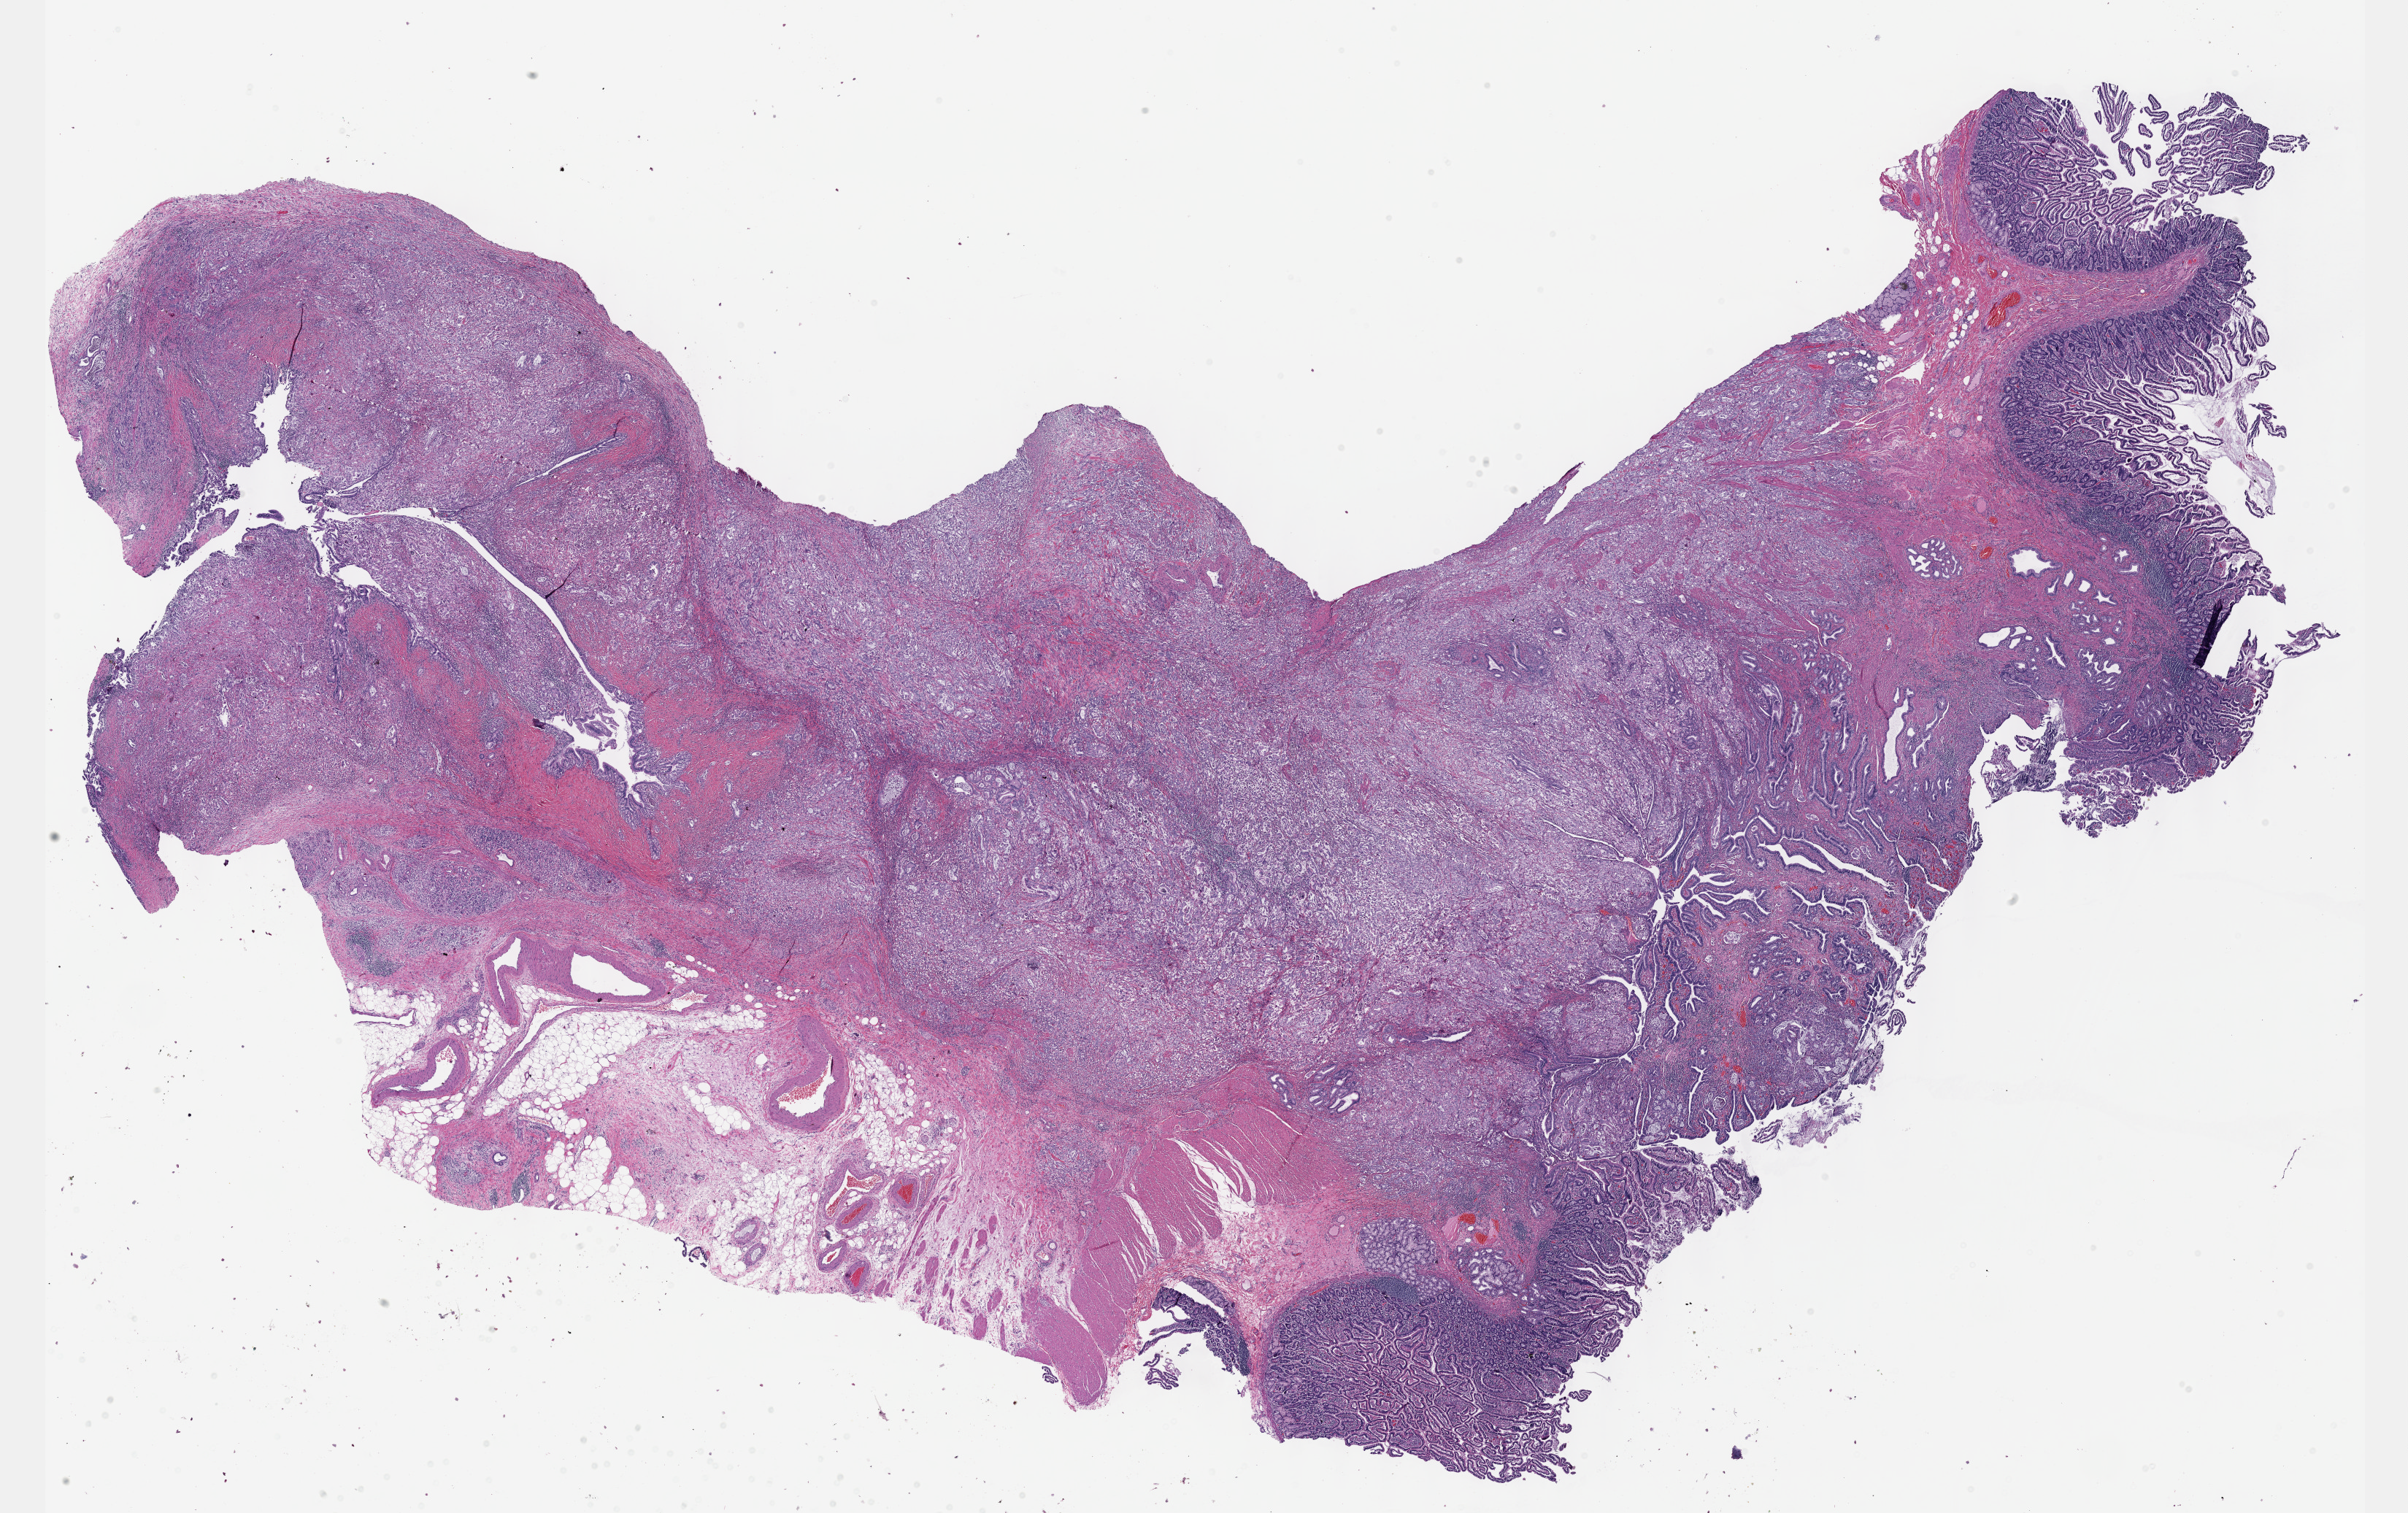
H&E whole-slide image — a low-resolution overview of the entire scanned area, about 26.7 x 16.8 mm (from a 40x scan). FFPE section. Sample: primary tumour, pancreas. Female patient; age at initial diagnosis 63 years. Histologic grade: G3 (poorly differentiated).
Lymph nodes positive (case pathology): 3 of 12 examined. AJCC pathologic stage: IIB (7th edition). Histologic diagnosis: Infiltrating duct carcinoma, NOS (head of pancreas). TNM: T3 N1 MX.